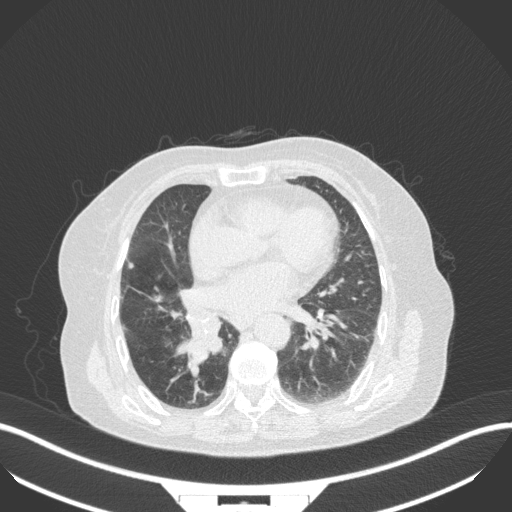
Chest CT, one axial slice; position 141 of 329 along the scan axis; 120 kVp; lung window (W 1500 / L -600 HU); 512 × 512 image matrix, field of view 400 × 400 mm. Patient: female, 75 years. Case-level facts recorded for this patient, not image findings: clinical TNM (as recorded): T1b N0 M1a.
Outlined on this slice (rectangle marked by the reading radiologist):
- lung tumour (recorded histology: squamous cell carcinoma): bounding box <170,314,226,371> (left, top, right, bottom; pixels)